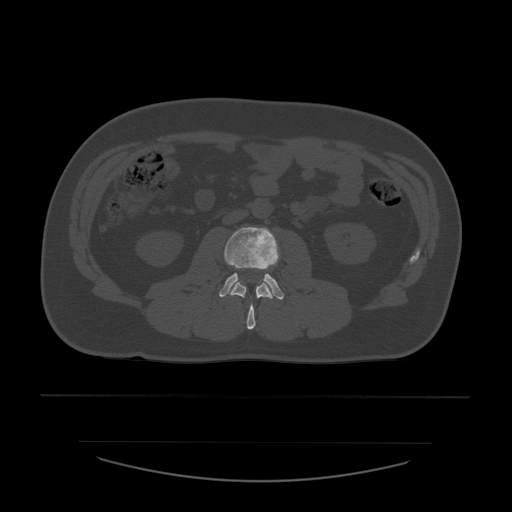
CT including the spine, one axial slice; position 185 of 532 along the scan axis; 120 kVp; bone window (W 1800 / L 400 HU); 1.25 mm slice thickness; 512 × 512 image matrix. Patient age 44 years. Case-level facts recorded for this patient, not image findings: primary cancer: soft tissue sarcoma.
Annotated regions visible in this slice (semi-automatically segmented with operator editing):
- L2 vertebra: bounding box (x1, y1, x2, y2) in pixels: (230, 282, 274, 330)
- L3 vertebra: (219, 227, 285, 300)